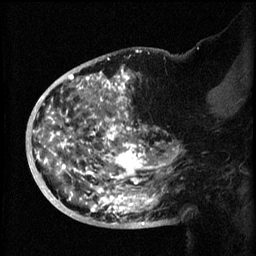
Breast MRI (dynamic contrast-enhanced), one sagittal slice. Position 33 of 60 along the scan axis. 3 images stored at this slice position (order not interpretable as contrast timing). 1.5 T. TE 4.2 ms, TR 8.2 ms. 2 mm slice thickness. 256 × 256 image matrix, field of view 200 × 200 mm. Female patient, age 50 years.
Annotated regions visible in this slice (semi-automatically segmented with operator editing):
- analysis volume of interest (the breast-tissue region the enhancement analysis was run in; not a lesion): bounding box (x1, y1, x2, y2) in pixels: (44, 72, 173, 219)
- tumour enhancement mask (voxels above the 70 % enhancement threshold inside the analysis volume of interest): (44, 72, 167, 219)